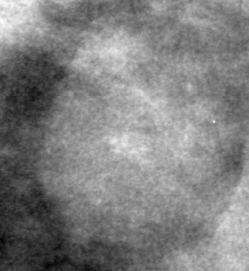
Cropped region of a digitized screen-film mammogram centred on a radiologist-marked abnormality; left breast; CC view.
Finding: mass, shape oval, margins obscured; BI-RADS assessment category 3; pathology result (as recorded, not read from the image): benign.